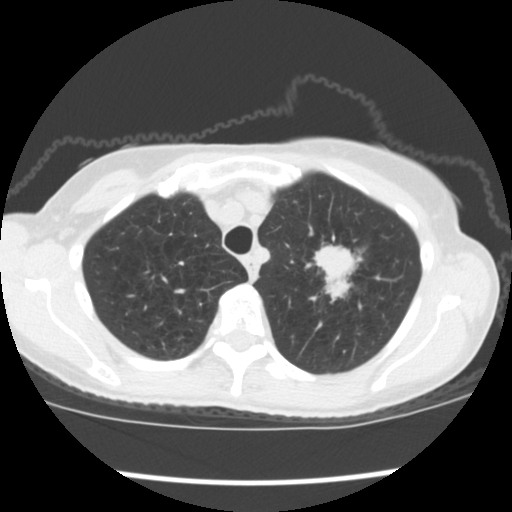
Axial slice from a low-dose chest CT screening exam. First (baseline) screen. Lung window (W 1500 / L -600 HU). 2.5 mm slice thickness. Slice 29 of 176 in the series. 512 × 512 image matrix, field of view 318 × 318 mm. Female participant, aged 67 years at enrolment. Former smoker at enrolment.
- Lesion marked by an expert reader, box from (x=303, y=236) to (x=375, y=310) px.
- Screening reader's record for this exam (one nodule recorded; not confirmed to be the boxed lesion): non-calcified nodule or mass ≥4 mm, left upper lobe, 34 × 32 mm, spiculated (stellate) margins, soft tissue attenuation, pre-existing on the prior screen: no.
- Official screen result: positive, change unspecified: nodule(s) >= 4 mm or enlarging nodule(s), mass(es), or other non-specific abnormalities suspicious for lung cancer.
- Later outcome: lung cancer diagnosed 17 days after this screen — small cell carcinoma, NOS, left upper lobe, stage IIIA (AJCC 6th edition), 40 mm at pathology.